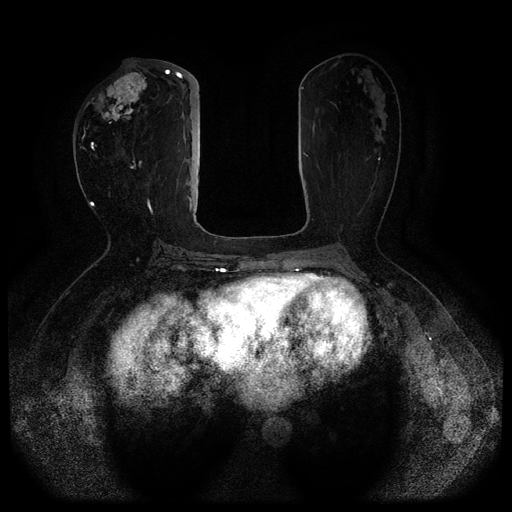
Breast MRI (dynamic contrast-enhanced, multi-phase), one axial slice. Slice 41 of 116 in the series (ordered by position). Dynamic contrast-enhanced series, time point 2 of 5 at this slice position (early post-contrast). 1.5 T. TE 2.6 ms, TR 5.3 ms. 2 mm slice thickness. 512 × 512 image matrix, field of view 350 × 350 mm. Patient: female, 51 years.
Outlined on this slice (semi-automatically segmented with operator editing):
- breast lesion (labelled 'tumour' in the annotation; benign lesions carry a separate 'benign' label): bounding box (x1, y1, x2, y2) in pixels: (87, 72, 147, 124)